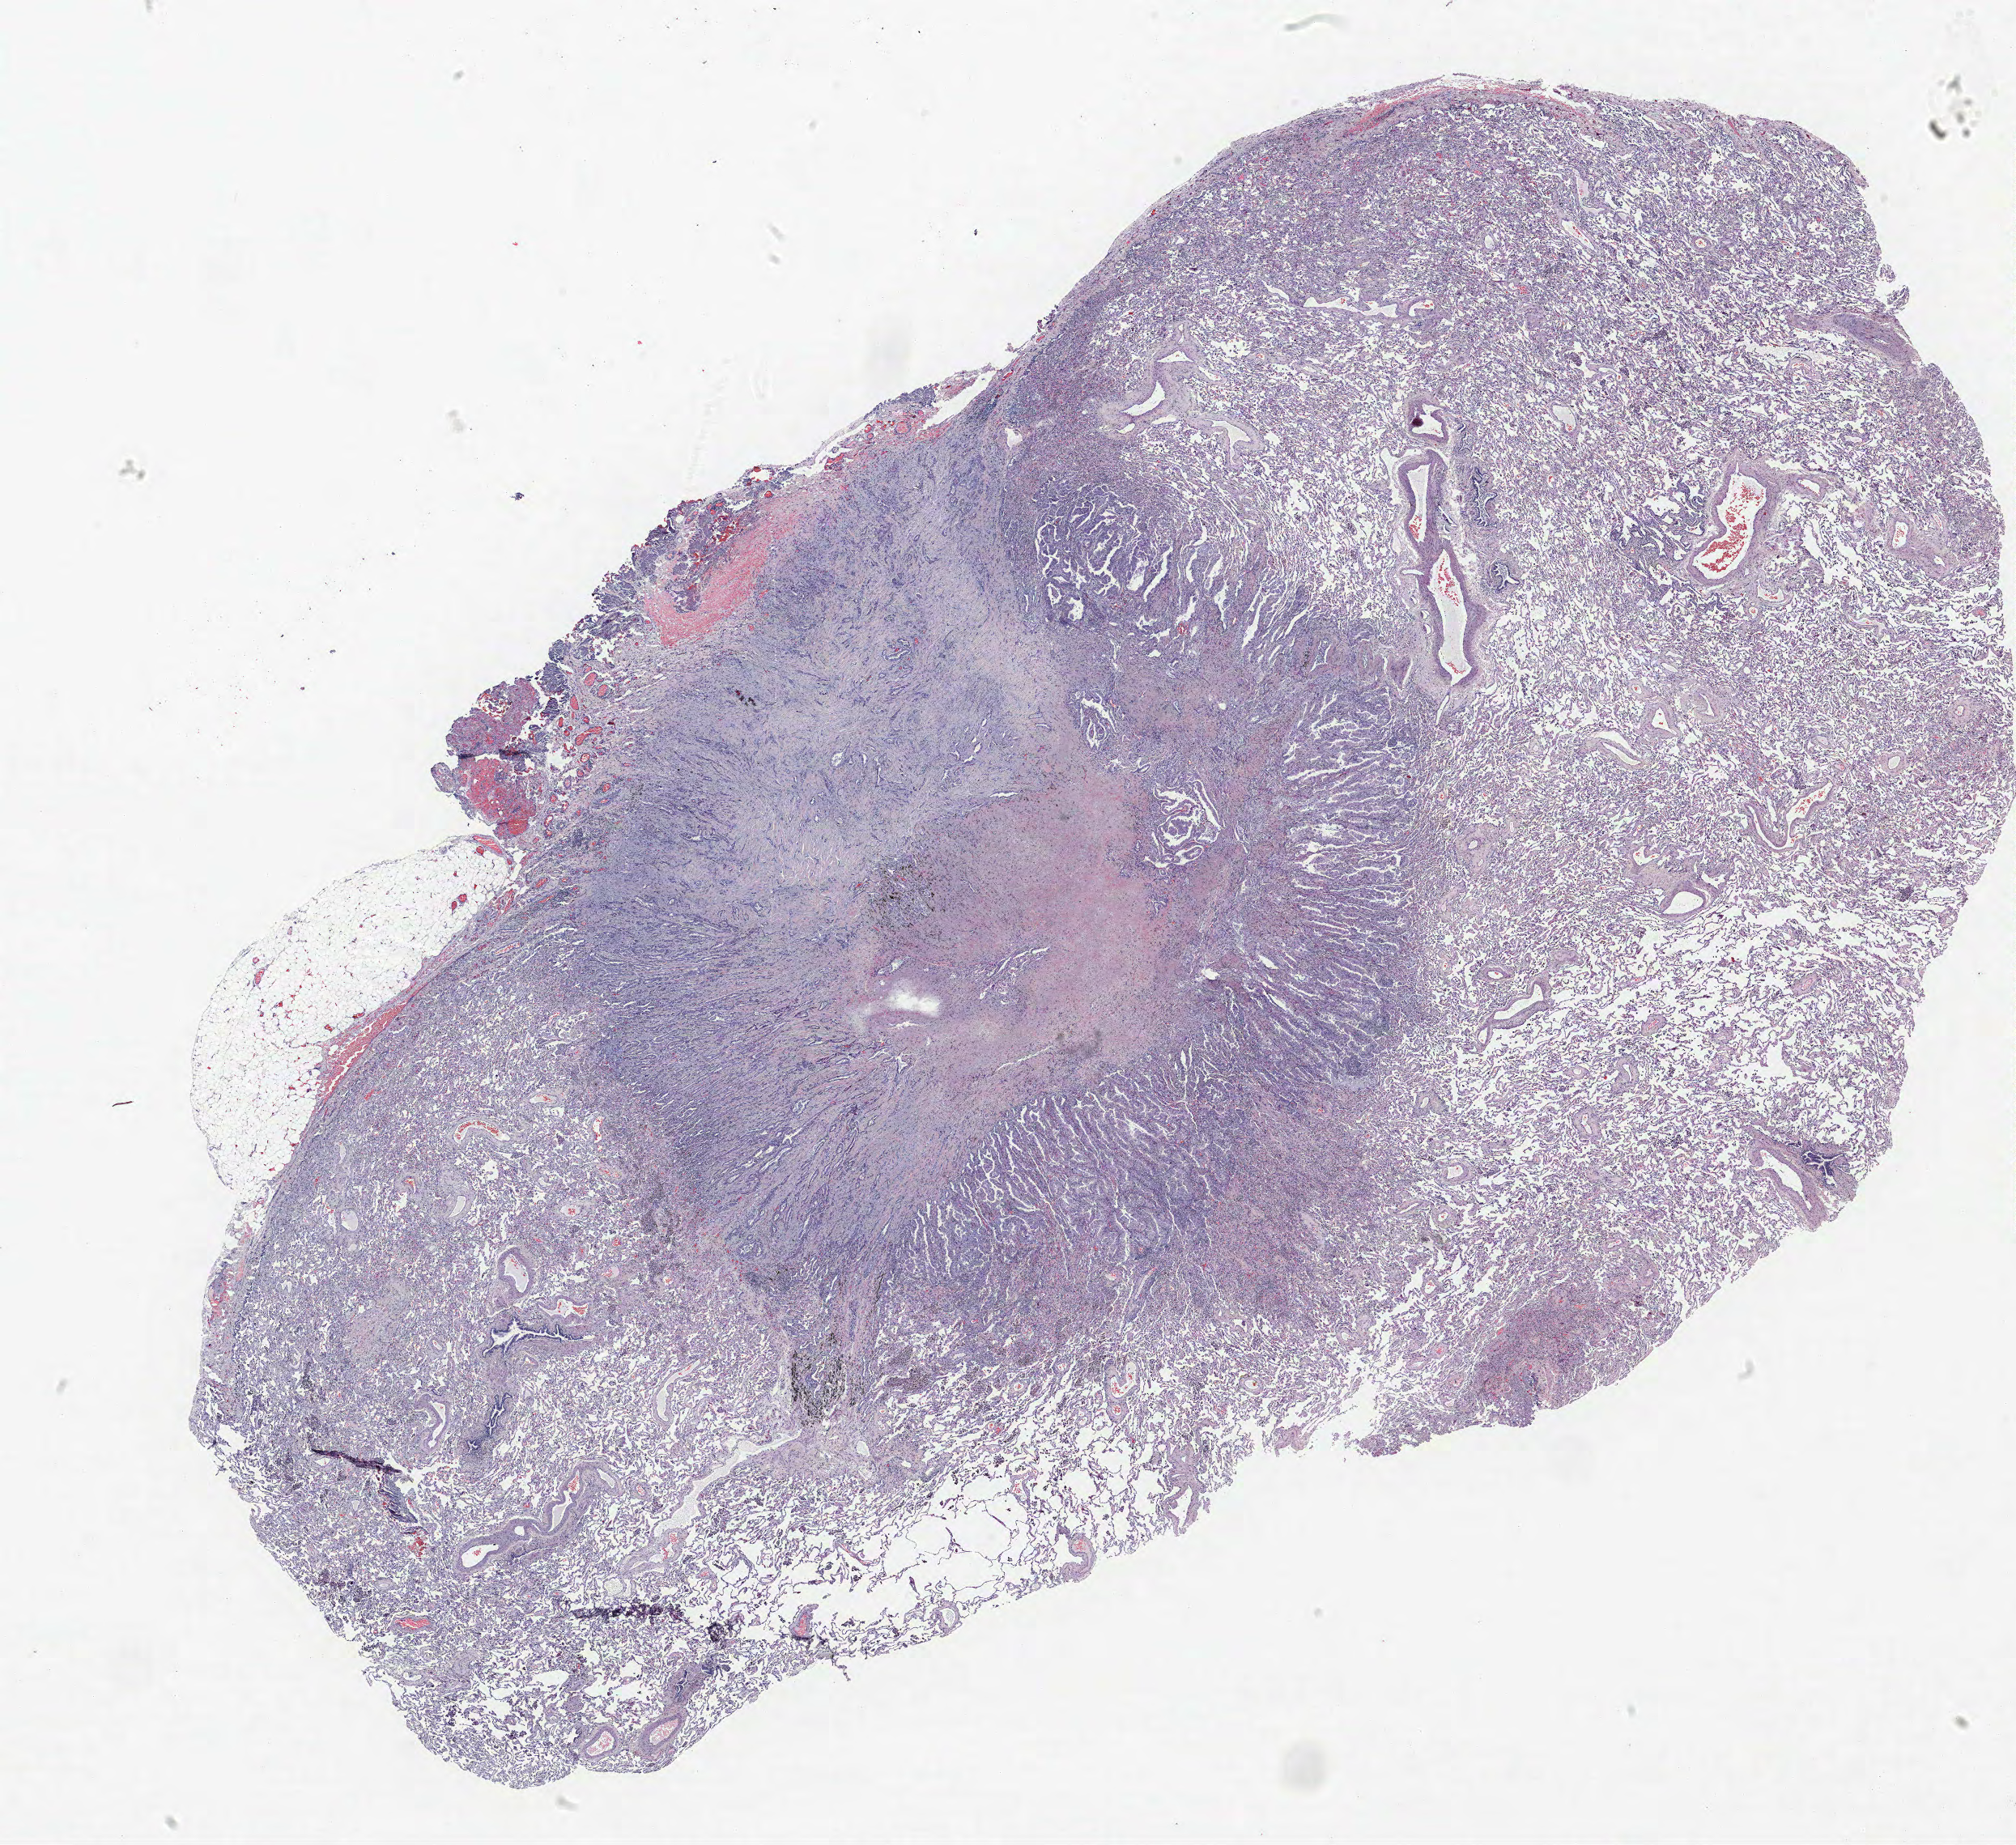
Whole-slide histology image, H&E-stained, low-resolution overview of the scanned area, about 19.9 x 18.2 mm (slide scanned at 40x). FFPE section. Lung. Male, age 68 at enrolment. Current smoker at enrolment. Grade: well differentiated (G1).
• stage (AJCC 6th edition): IV
• primary tumour location (clinical record): right upper lobe, right lower lobe
• tumour size (pathology): 35 mm
• participant's lung-cancer diagnosis: Adenocarcinoma, NOS (ICD-O-3 8140/3)